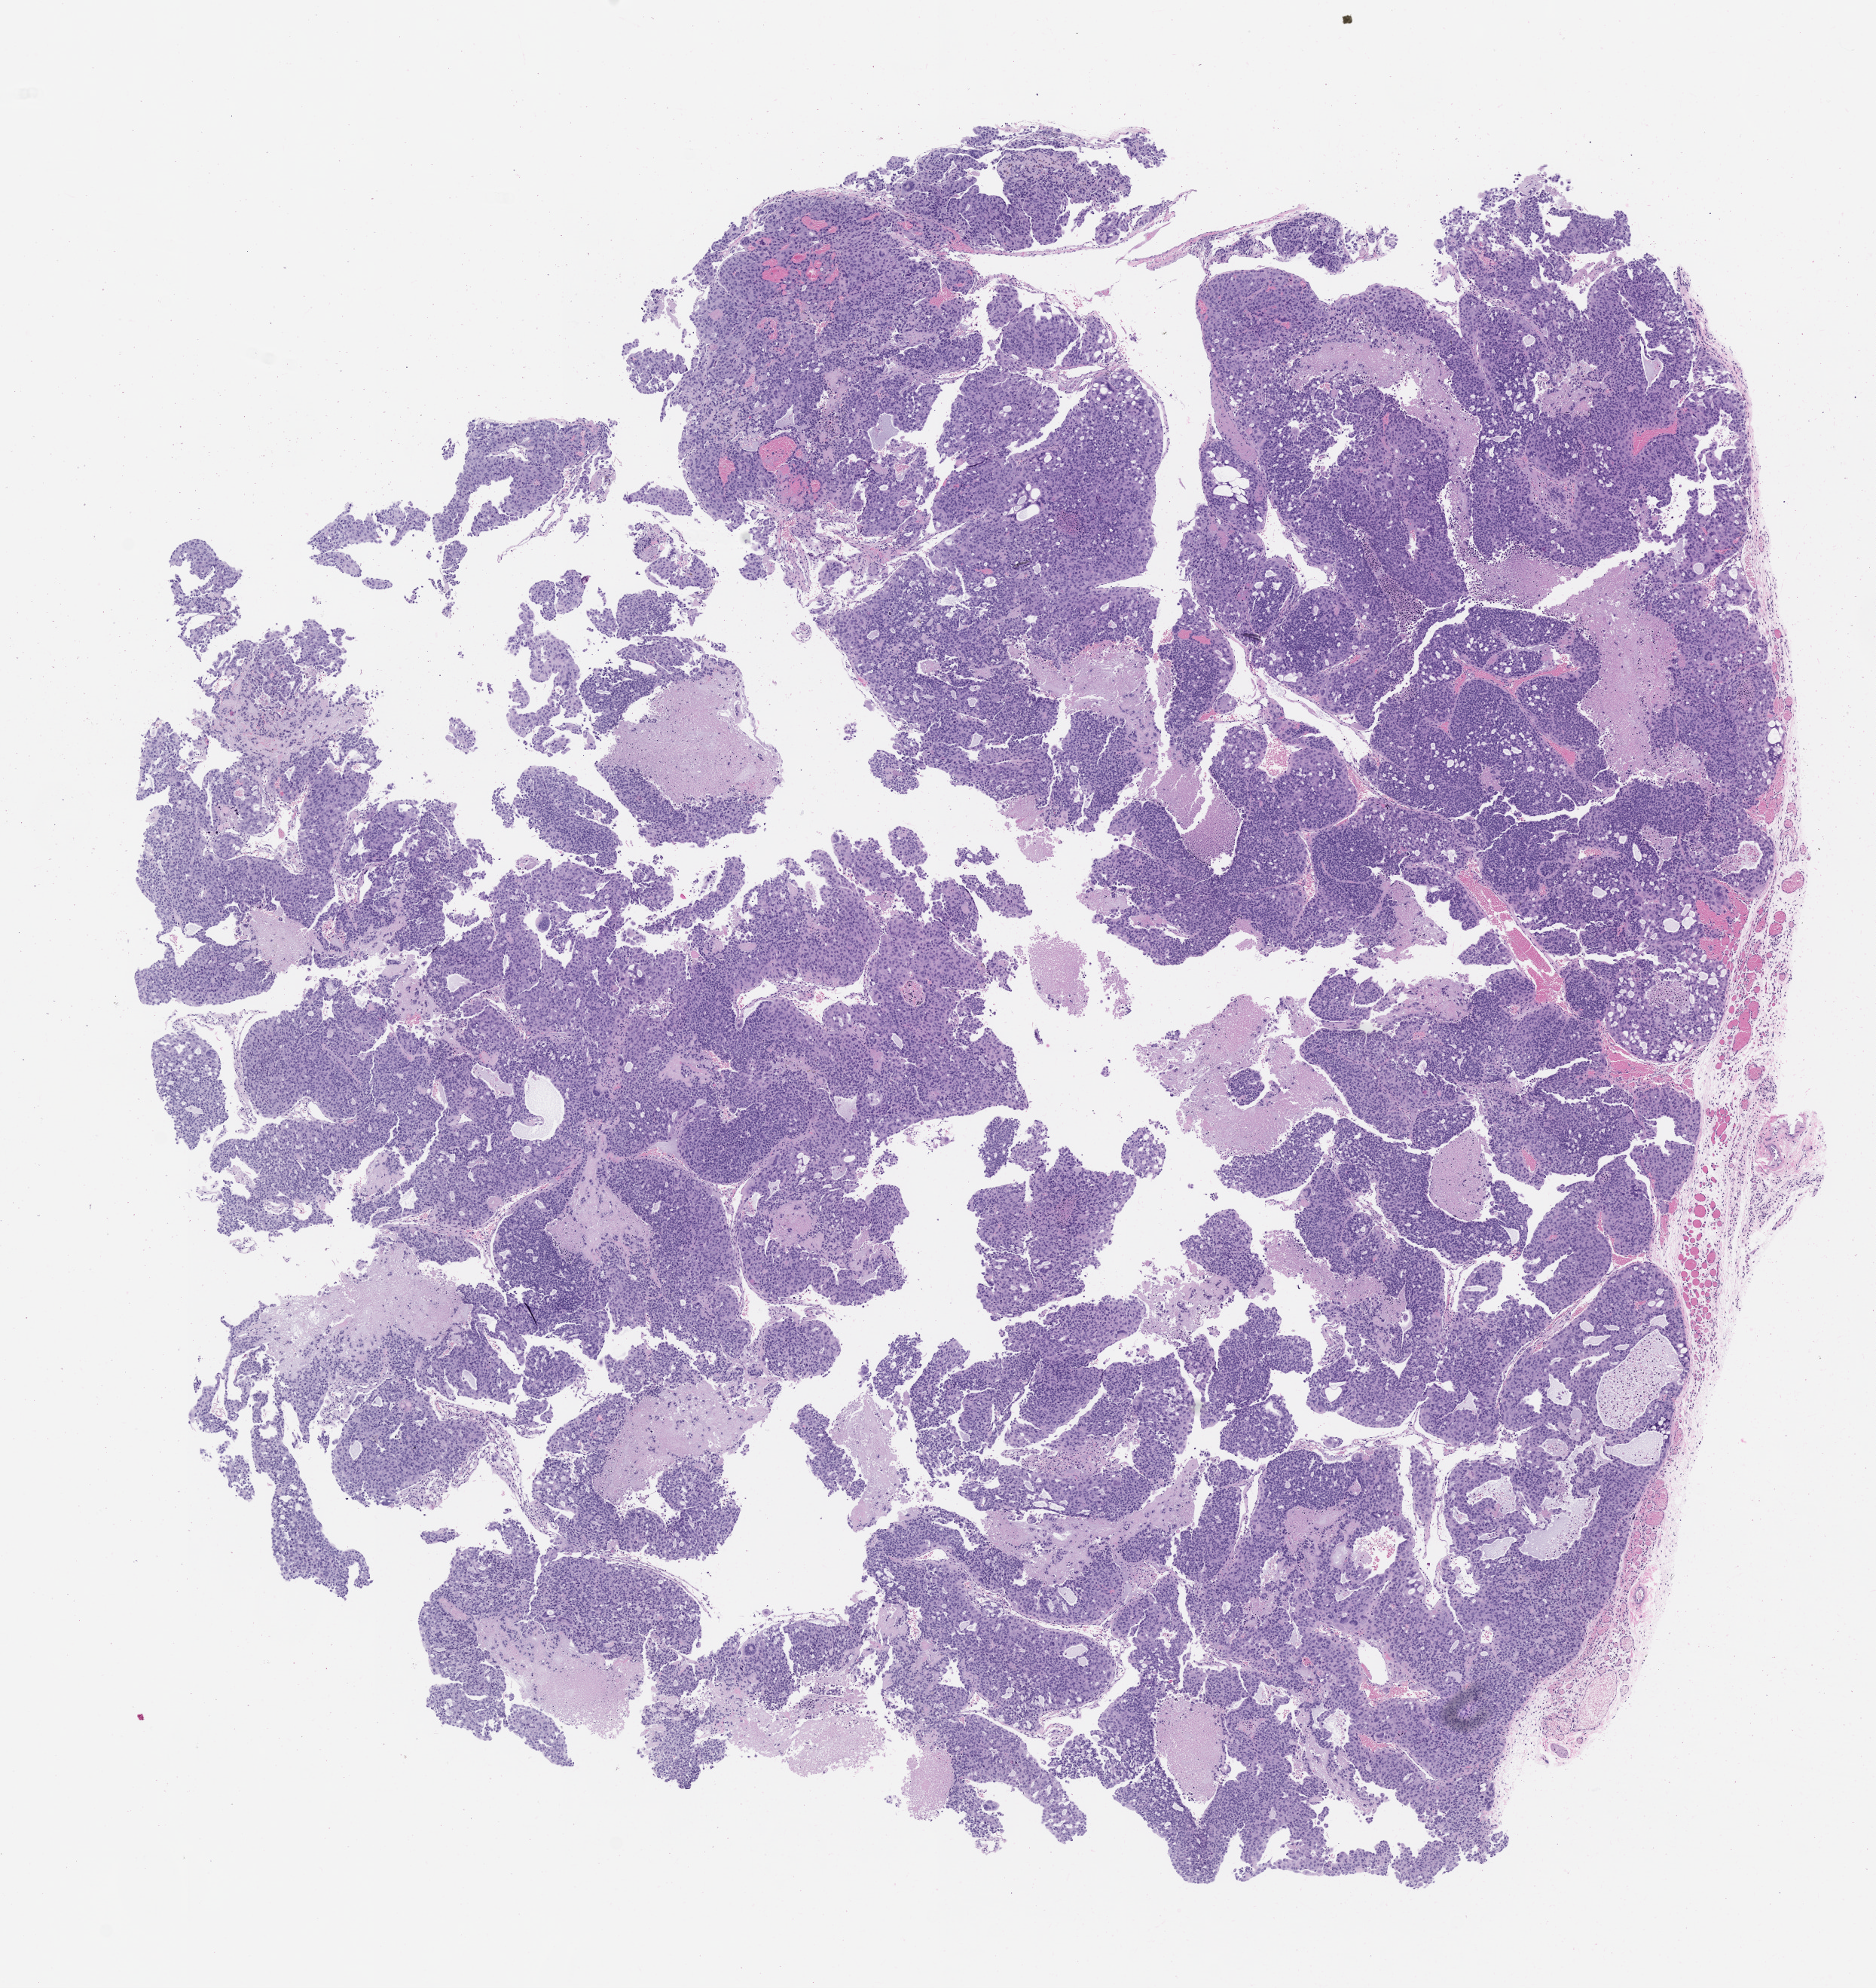
Whole-slide image, haematoxylin and eosin: patient-derived xenograft (human tumor grown in a mouse), passage 0 — whole scanned area (about 10.0 x 10.6 mm) shown as a low-resolution overview. Formalin-fixed, paraffin-embedded (FFPE) tissue. Tumor site category: bladder.
Originating patient diagnosis: Urothelial Carcinoma.